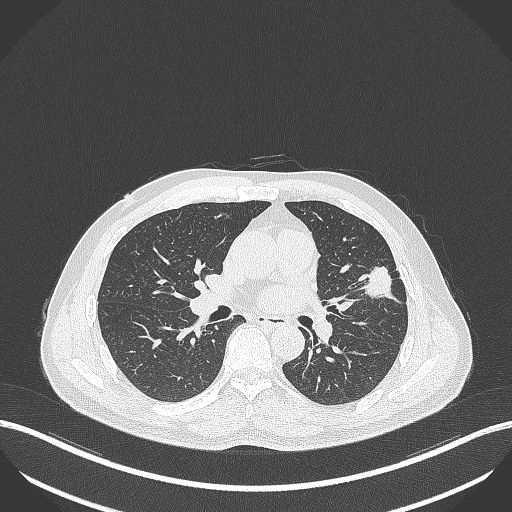
Chest CT, one axial slice. Position 216 of 418 along the scan axis. Reconstruction kernel B70f. Lung window (W 1500 / L -600 HU). 1 mm slice thickness. 512 × 512 image matrix. Male patient, age 55 years. From the clinical record (not read from this slice): clinical TNM (as recorded): T1c N0 M0.
Structures marked on this image (rectangle marked by the reading radiologist):
- lung tumour (recorded histology: adenocarcinoma): box from (x=361, y=264) to (x=400, y=305) px